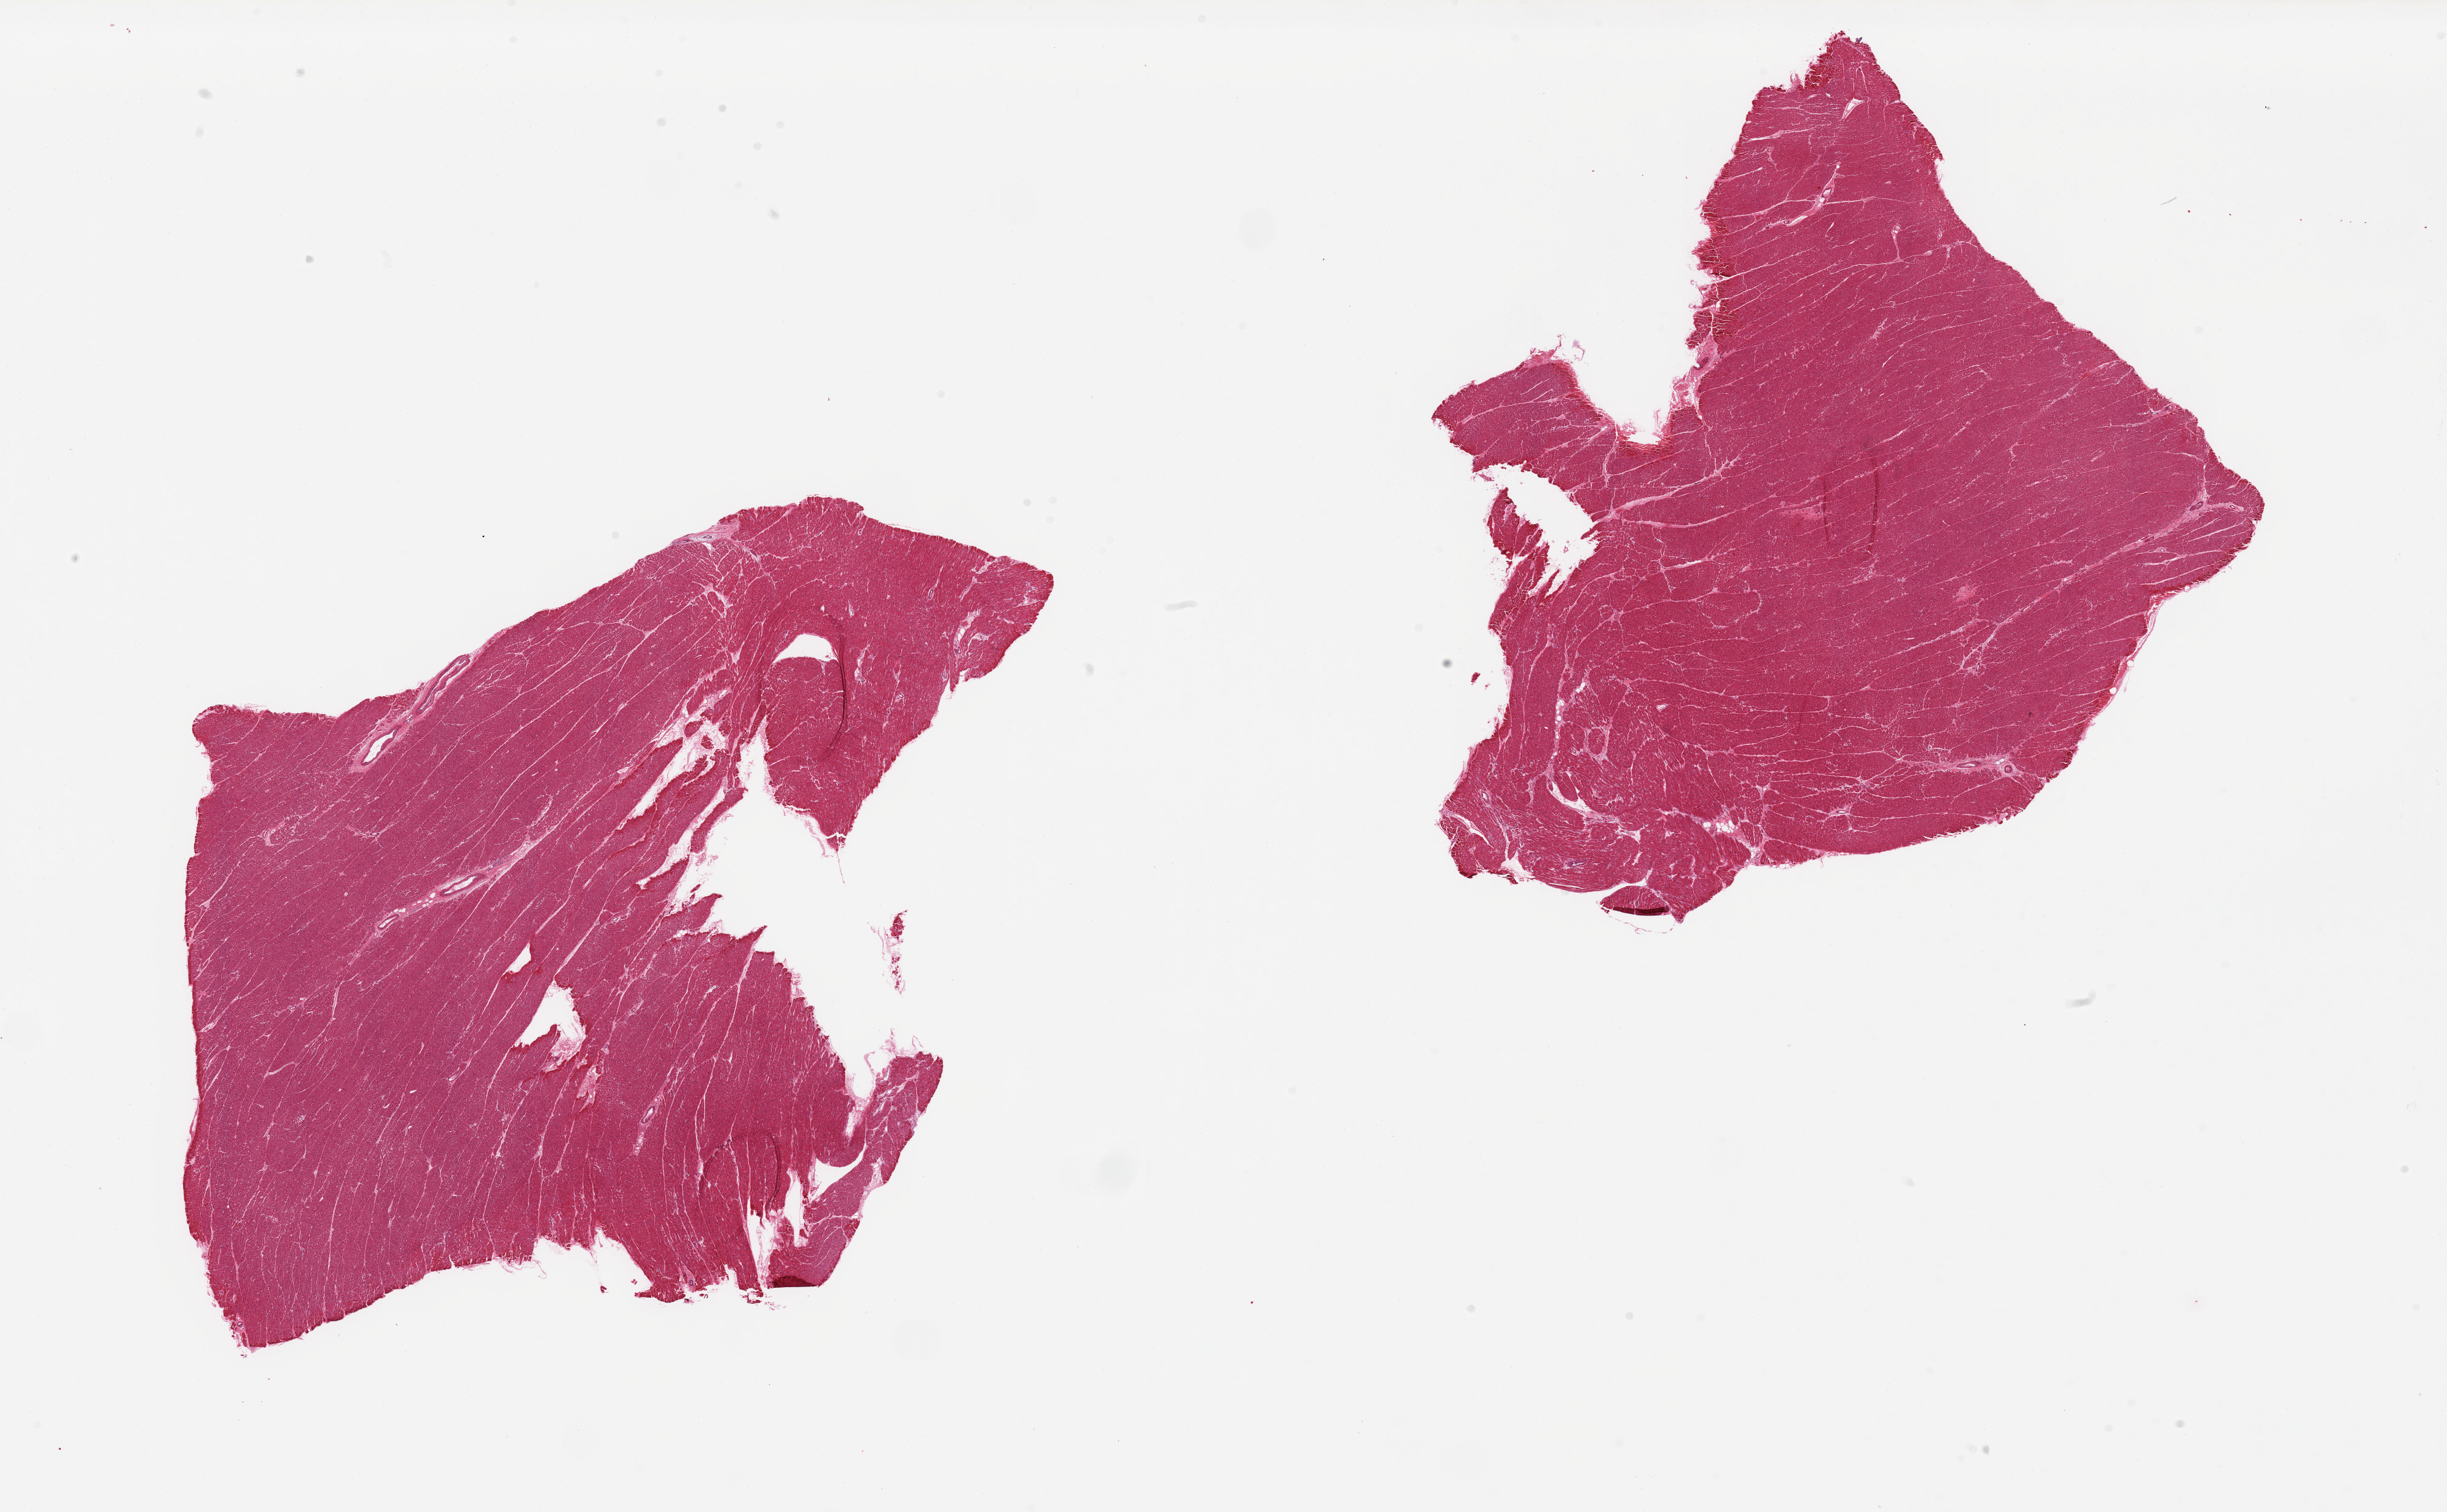
Digitized haematoxylin and eosin-stained section, brightfield, low-resolution overview of the scanned area, about 31.5 x 19.5 mm, PAXgene-fixed, paraffin-embedded tissue, target tissue: heart, tissue donor sample. Donor sex: male.
Review note (as recorded): 2 pieces, patchy mild-moderate intersitital fibrosis, micro infarct noted.